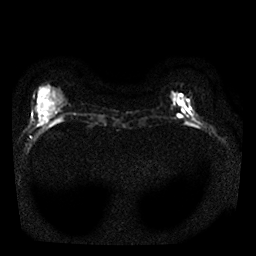
Breast MRI, one axial slice. Position 5 of 25 along the scan axis. Diffusion-weighted series; image 2 of 4 stored at this slice position (different b-values; order by instance number). 1.5 T. 4 mm slice thickness. 256 × 256 image matrix, field of view 320 × 320 mm. Female patient.
Annotated regions visible in this slice (outlined manually by an expert reader):
- tumour on diffusion-weighted imaging: box from (x=178, y=114) to (x=182, y=117) px